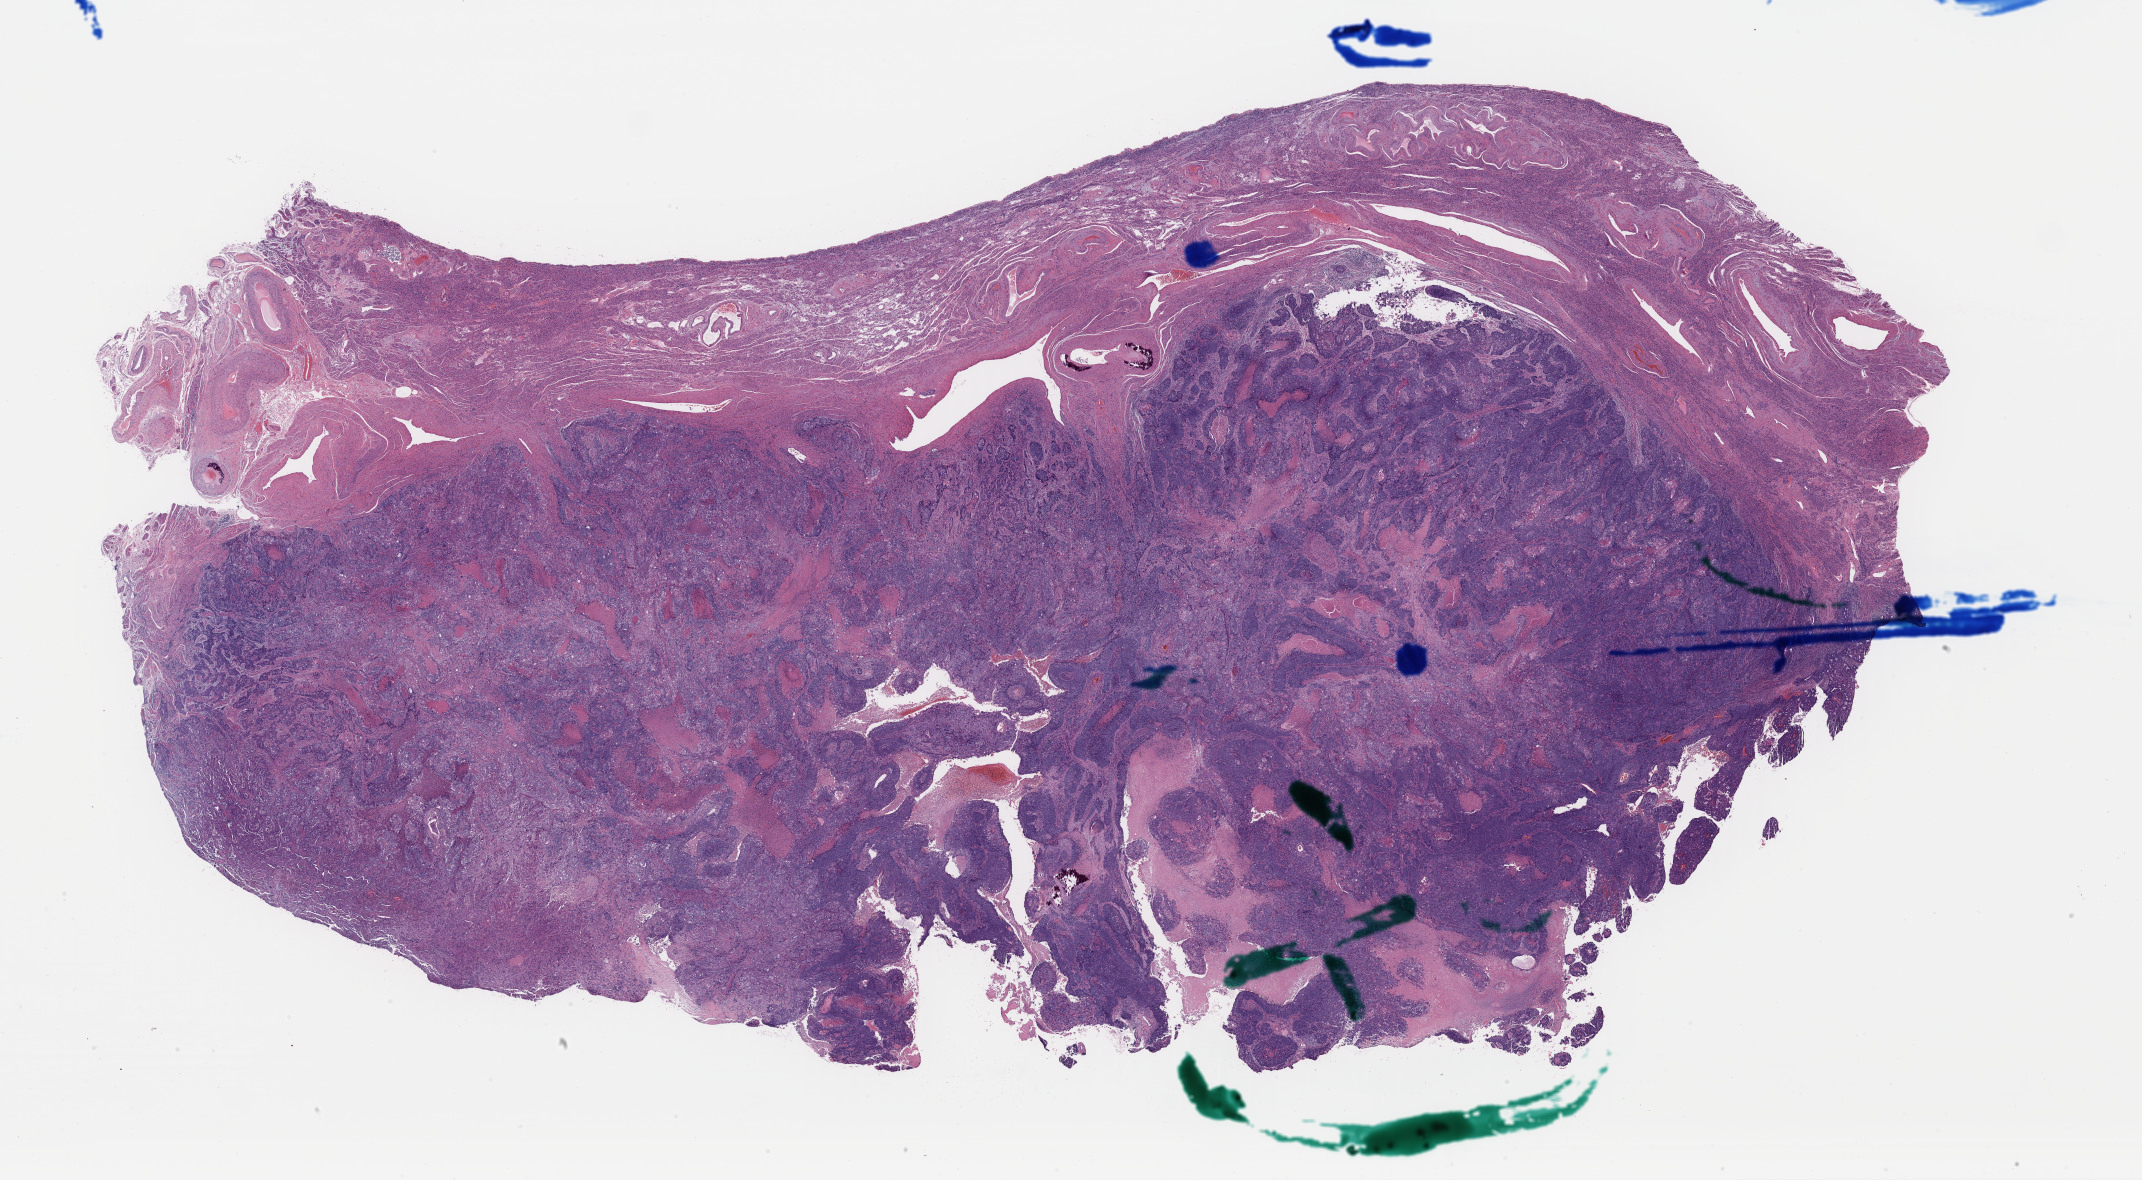
Hematoxylin and eosin (H&E) stained whole-slide image — shown as a low-resolution overview of the whole scanned area (about 33.8 x 18.6 mm, from a 40x scan), FFPE section, sample: primary tumour, uterus. Patient: female, age at initial diagnosis 84 years. Histologic grade: G3 (poorly differentiated).
FIGO stage: IB. Histologic diagnosis: Endometrioid adenocarcinoma, NOS (endometrium).